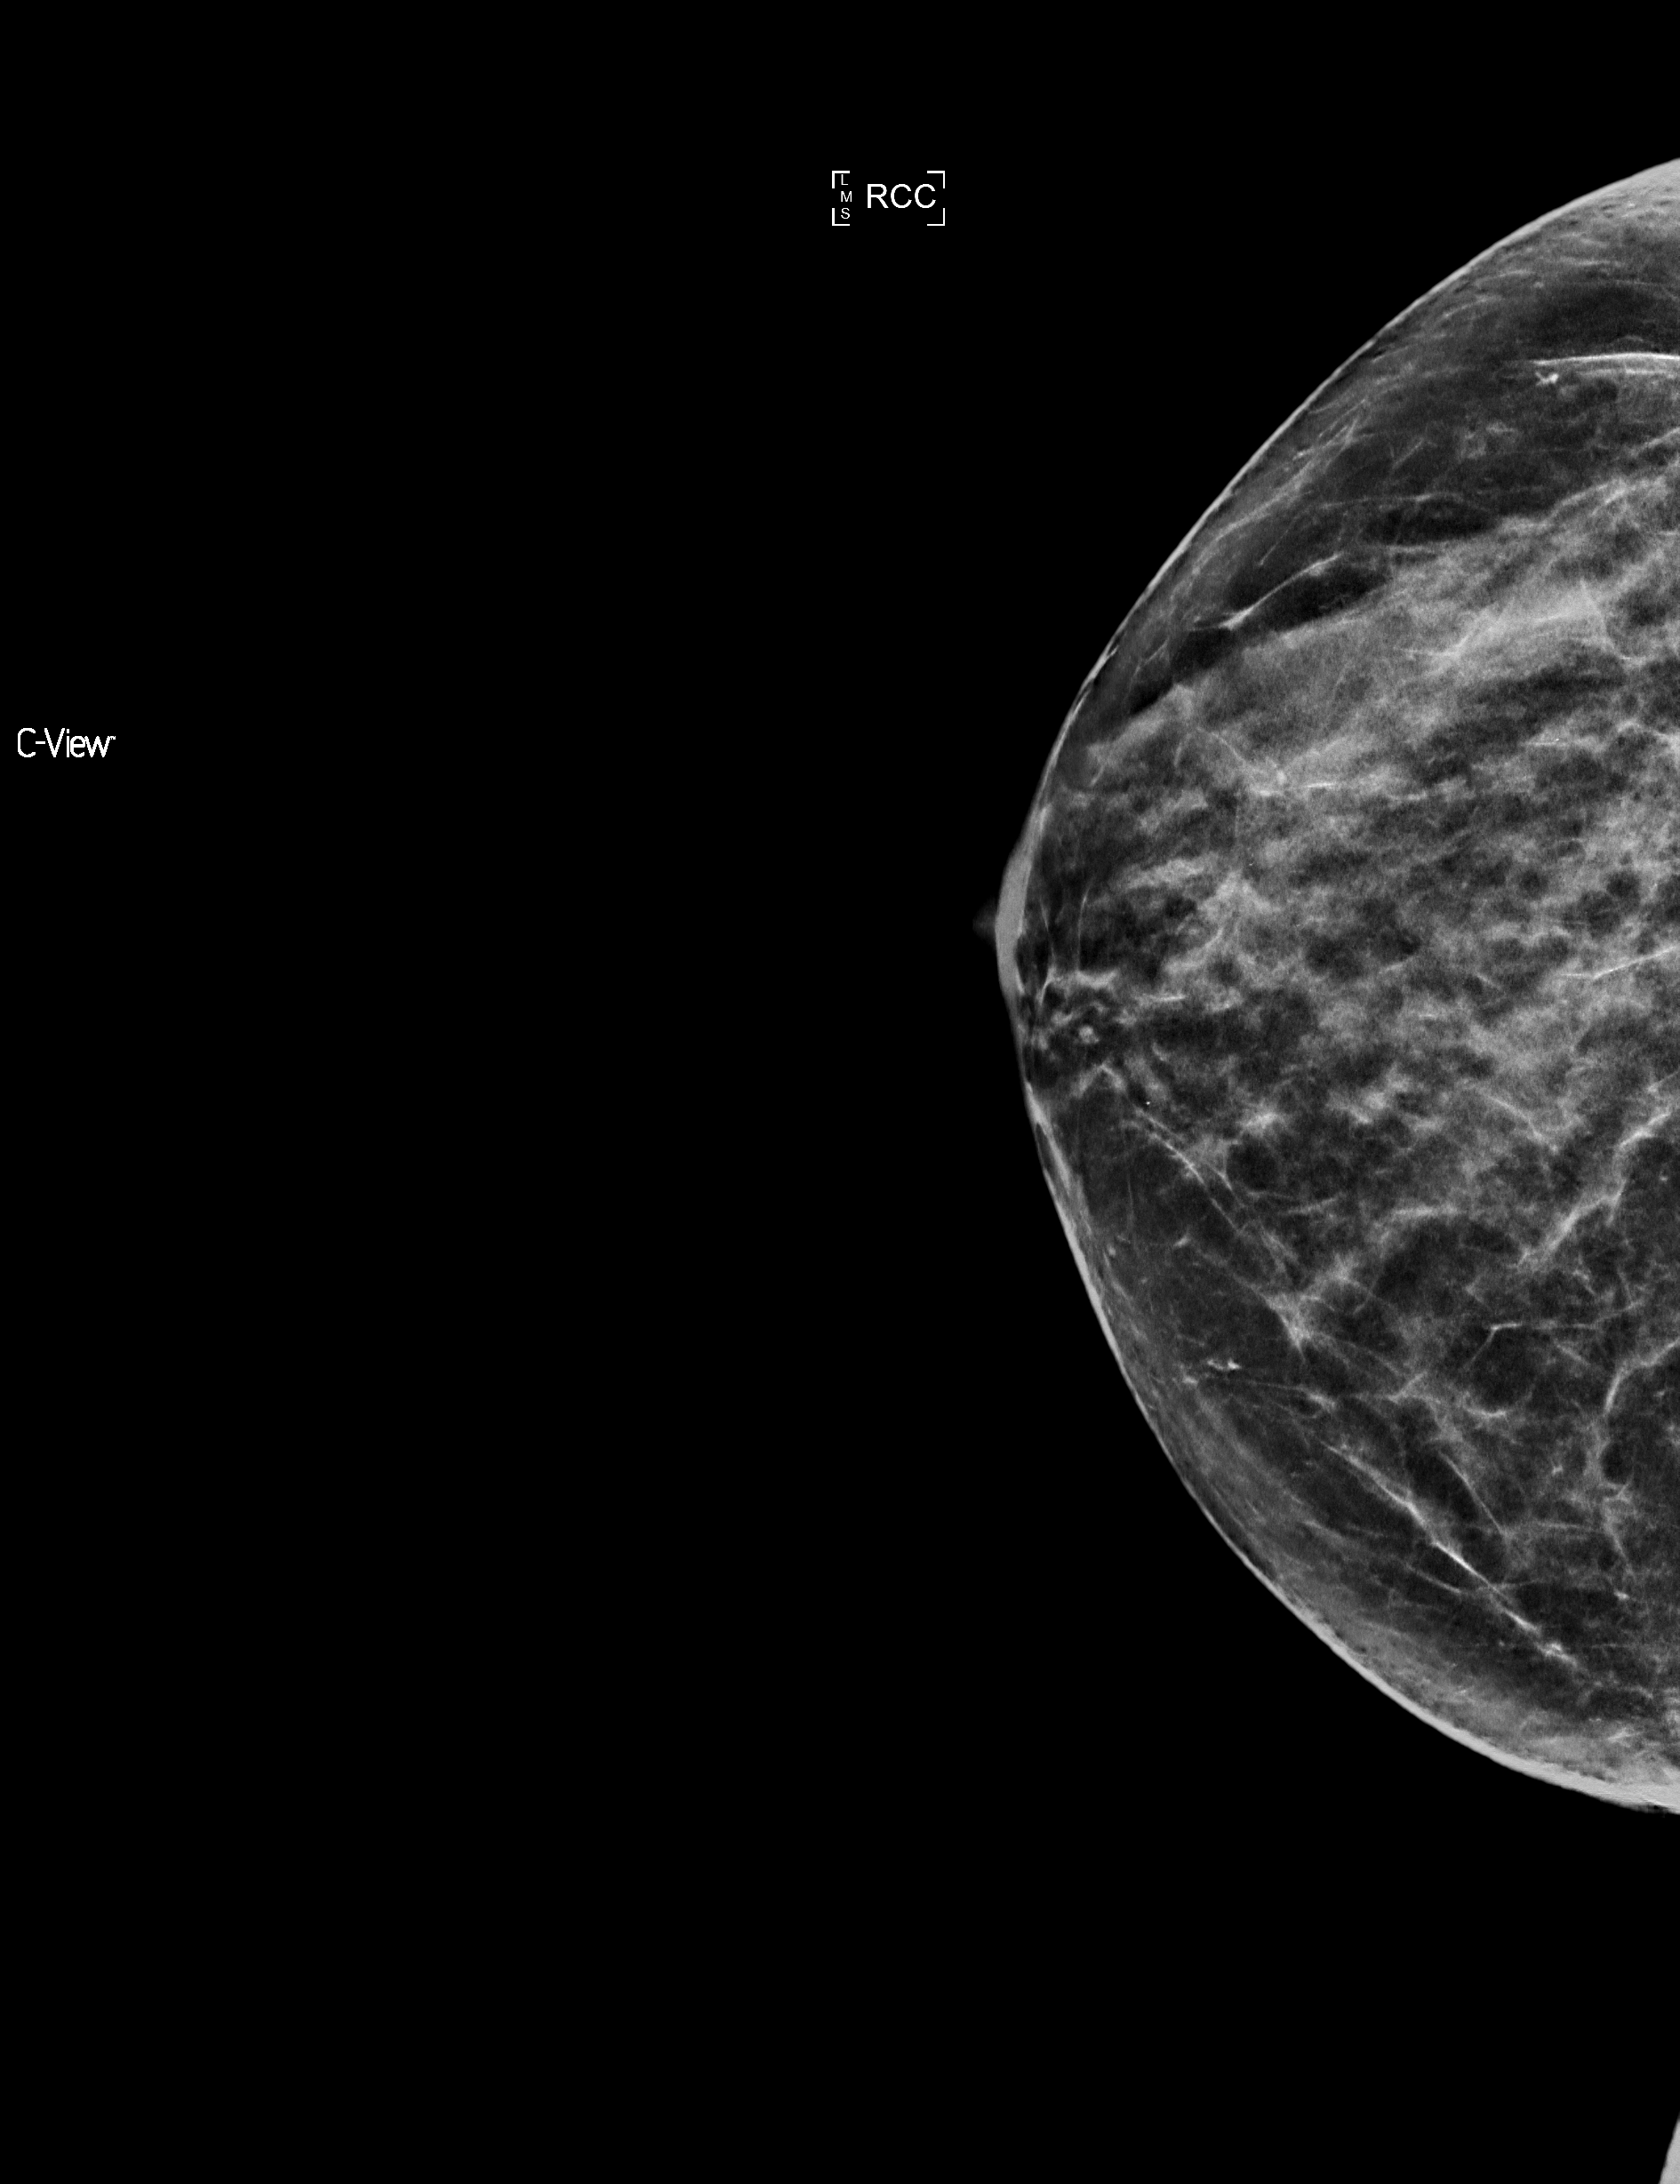
Digital mammogram (FFDM), right breast, CC view, annual screening mammography examination. Patient: female, 59 years.
BI-RADS breast density category at the screening exam (both breasts, scale 1–4): 3. Final BI-RADS assessment for this screening round (tomosynthesis exam, both breasts): category 1. Recall: no recall after this screen.